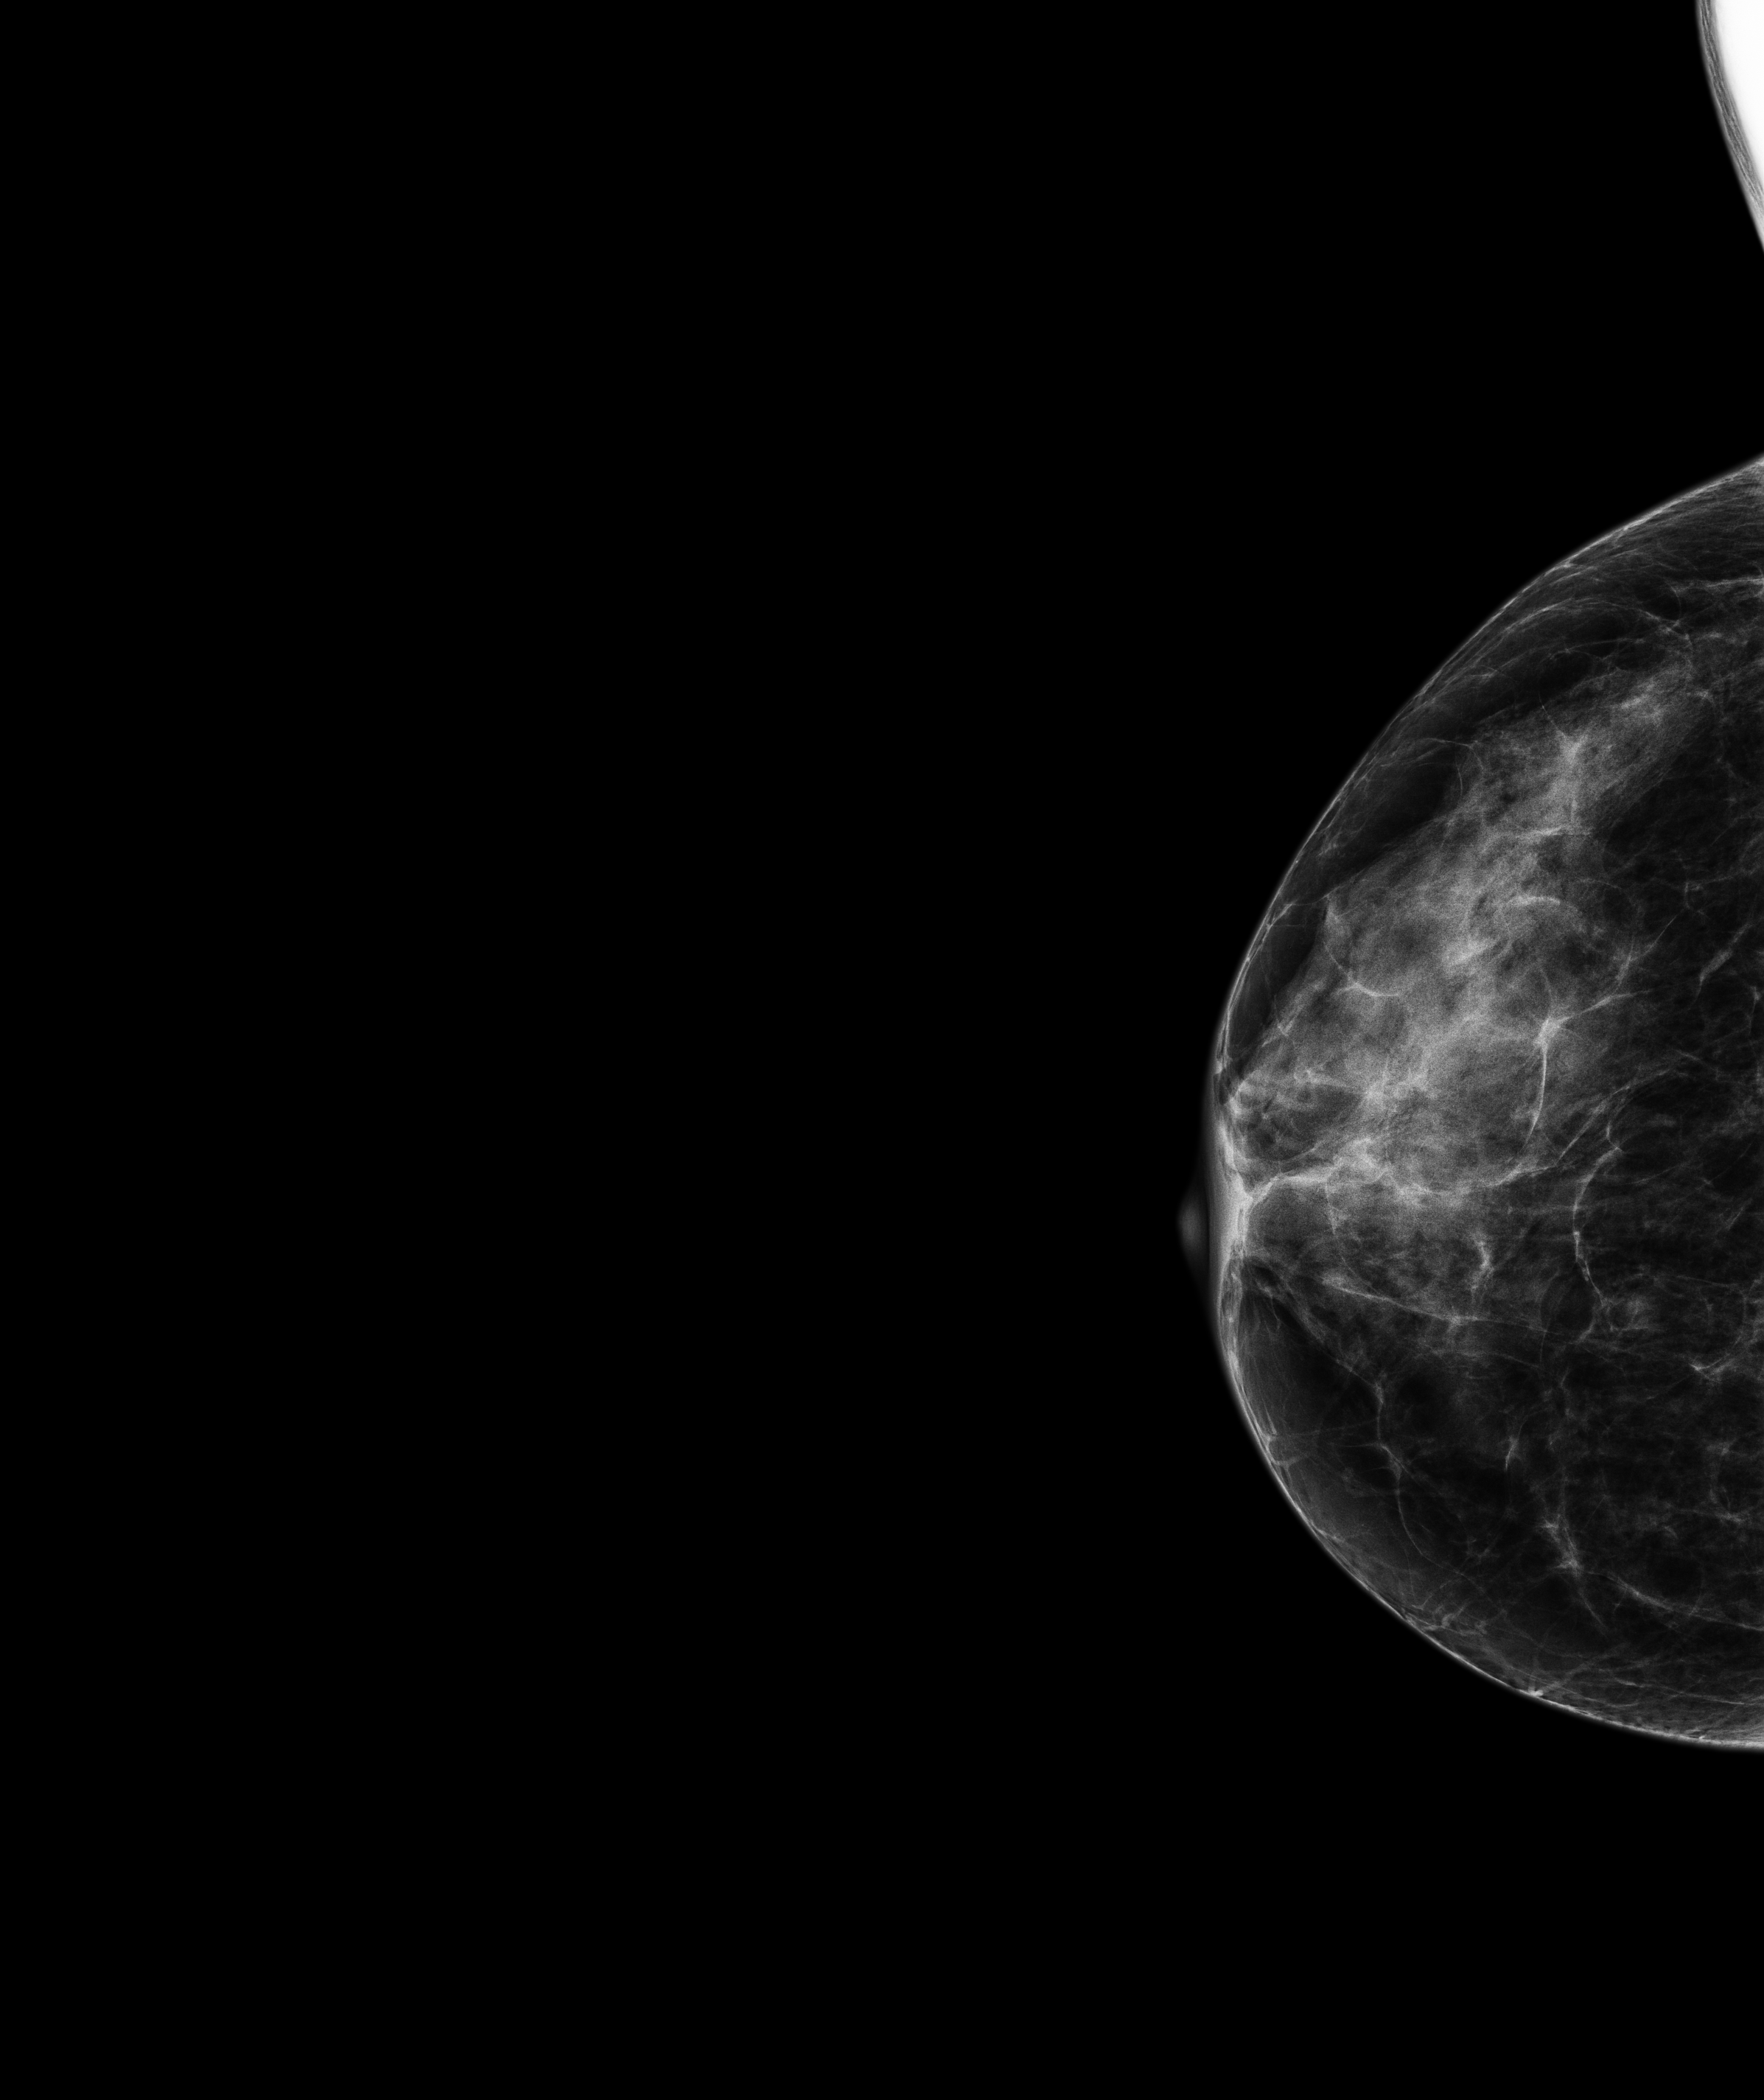
Digital mammogram (FFDM); right breast; CC view; annual screening mammography examination; compressed breast thickness 25.7 mm; system: Senographe Pristina. Patient aged 47 years (female).
Breast density at the screening exam (both breasts): heterogeneously dense (BI-RADS density category c). Final BI-RADS category for the screening round (tomosynthesis exam, both breasts): category 2. Recall: no recall after this screen.